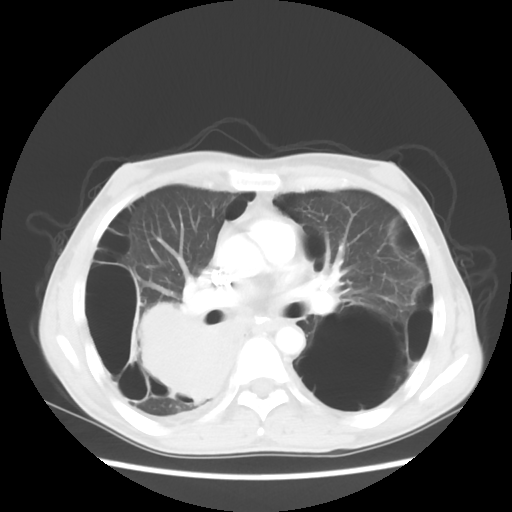
Chest CT, one axial slice; position 30 of 56 along the scan axis; reconstruction kernel STANDARD; 140 kVp; lung window (W 1500 / L -600 HU); 5 mm slice thickness; 512 × 512 image matrix, field of view 351 × 351 mm. Patient: male, 41 years. From the clinical record (not read from this slice): clinical TNM (as recorded): T4 N0 M1a.
Annotated regions visible in this slice (rectangle marked by the reading radiologist):
- lung tumour (recorded histology: large cell carcinoma): box from (x=117, y=298) to (x=262, y=412) px